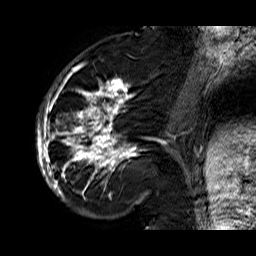
Breast MRI (dynamic contrast-enhanced), one sagittal slice. Position 22 of 60 along the scan axis. Dynamic contrast-enhanced series, time point 2 of 6 at this slice position (early post-contrast). 1.5 T. TE 6.3 ms, TR 32.9 ms. 256 × 256 image matrix. Female patient. Case-level facts recorded for this patient, not image findings: setting: breast cancer imaged before/during neoadjuvant chemotherapy; receptor status: HR-positive, HER2-negative.
Structures marked on this image (semi-automatically segmented with operator editing):
- analysis volume of interest (the breast-tissue region the enhancement analysis was run in; not a lesion): box from (x=36, y=74) to (x=176, y=210) px
- tumour enhancement mask (voxels above the 100 % enhancement threshold inside the analysis volume of interest): (x=36, y=74)–(x=176, y=202)